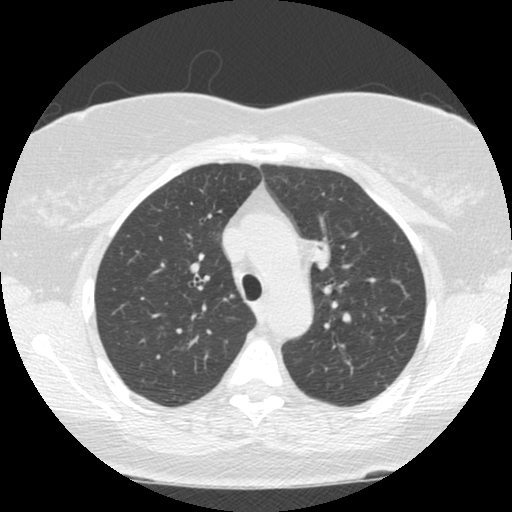
Low-dose screening chest CT, axial slice; second annual screen; lung window (W 1500 / L -600 HU); 2.5 mm slice thickness; standard (soft-tissue) reconstruction kernel (STANDARD); 512 × 512 image matrix. Female, age 66 years at enrolment.
Lesion marked by an expert reader, bounding box (x1, y1, x2, y2) in pixels: (290, 233, 344, 284). Screening reader's record for this exam (one nodule recorded; not confirmed to be the boxed lesion): non-calcified nodule or mass ≥4 mm, left upper lobe, 12 × 9 mm, smooth margins, soft tissue attenuation, pre-existing on the prior screen: no. Official screen result: positive, other. Participant outcome: lung cancer diagnosed 196 days after this screen — small cell carcinoma, NOS, left upper lobe, stage IIIA (AJCC 6th edition), 50 mm at pathology.